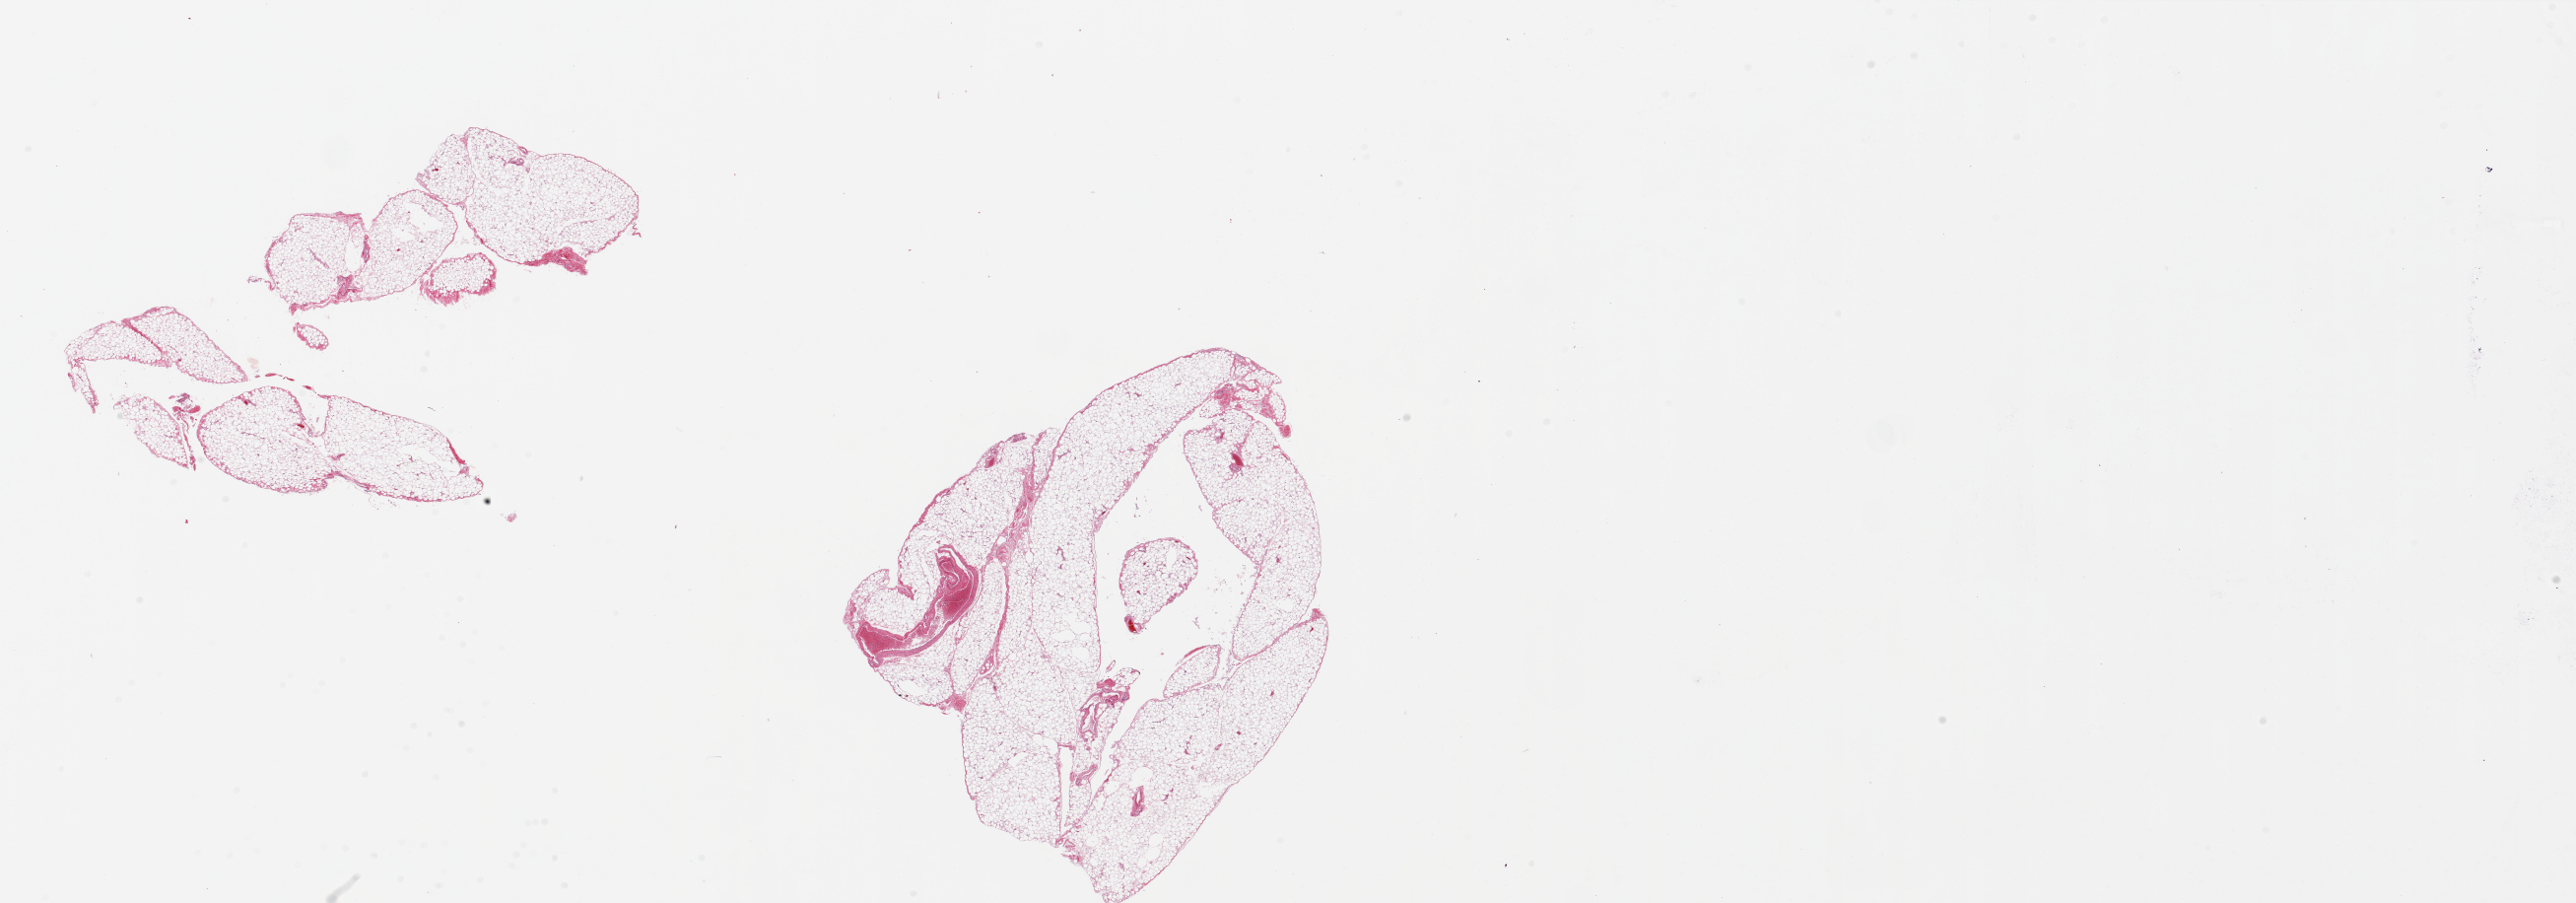
Whole-slide image, hematoxylin and eosin (H&E) stain, brightfield — a low-resolution overview of the entire scanned area, about 41.3 x 14.5 mm (from a 20x scan), PAXgene-fixed, paraffin-embedded tissue, sampled site (target tissue): omentum, tissue donor sample. Donor sex: female.
• reviewer comment on this tissue sample: 2 pieces, 9.5x8 & 8.5x7mm; well fixed